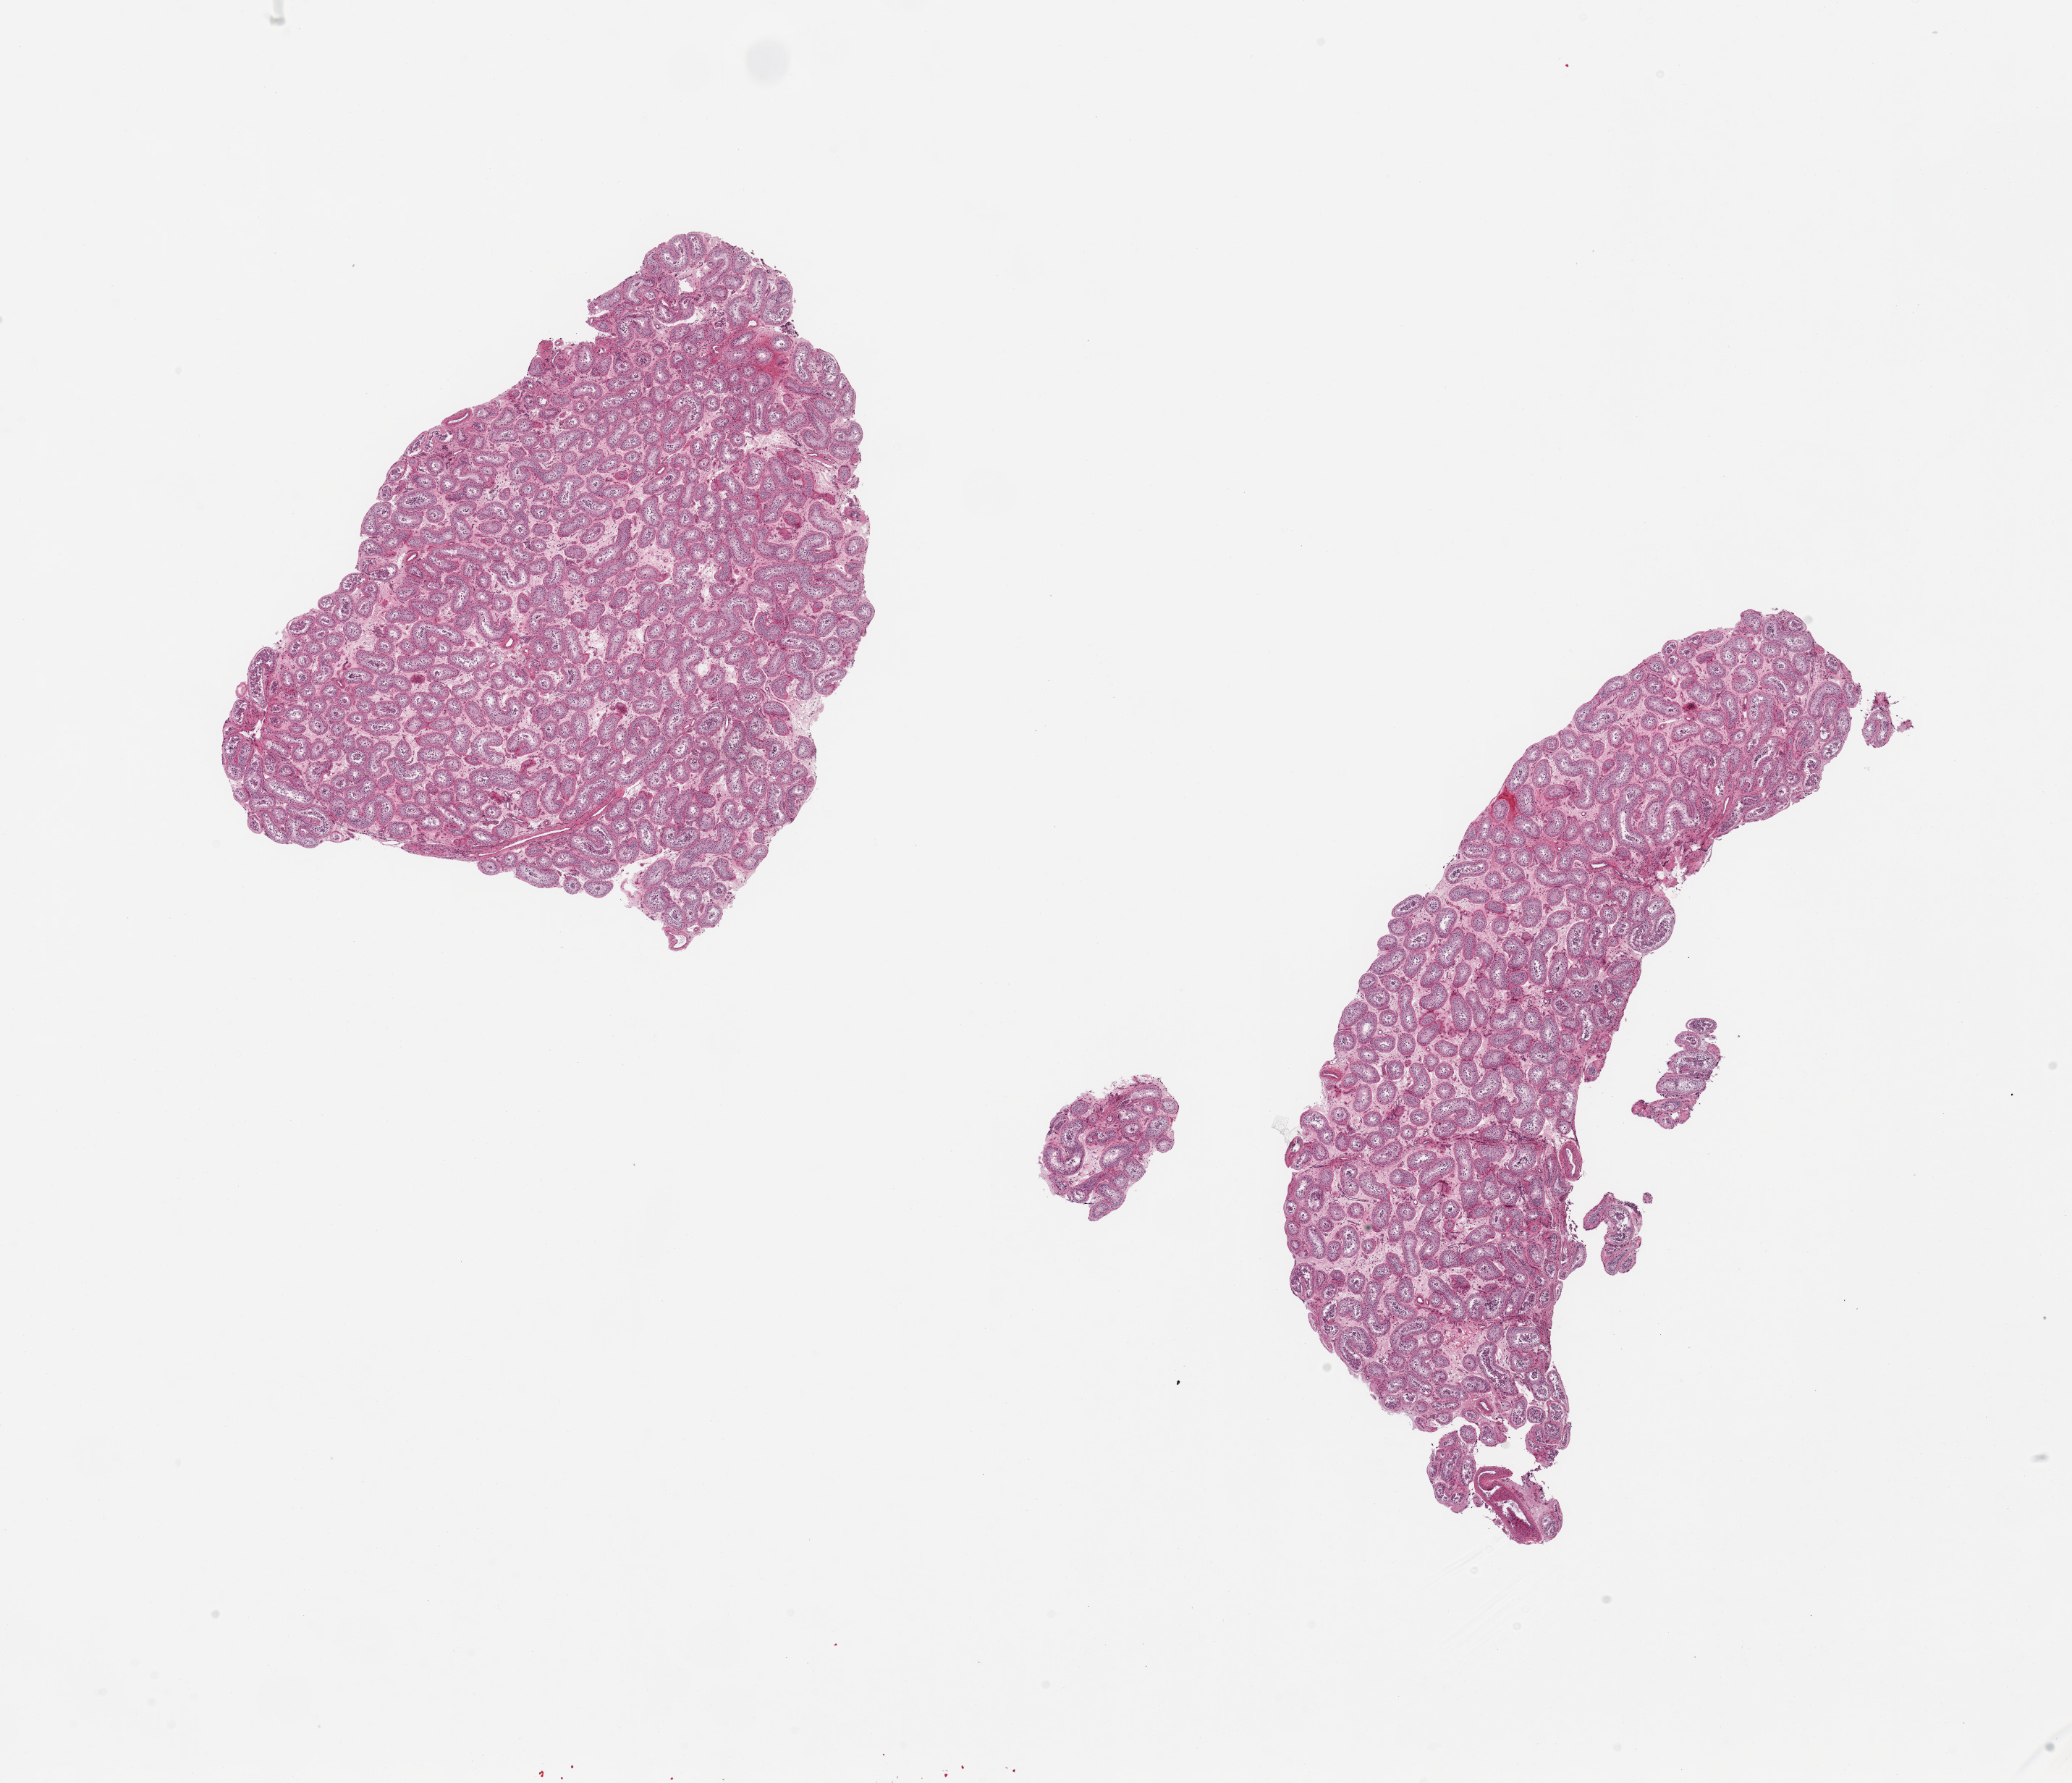
Haematoxylin and eosin whole-slide image, brightfield, low-resolution overview of the scanned area, about 22.6 x 19.5 mm, PAXgene-fixed, paraffin-embedded tissue, target tissue: testis, donor tissue sample.
Review note (as recorded): 2 pieces, spermatogenesis appears reduced.